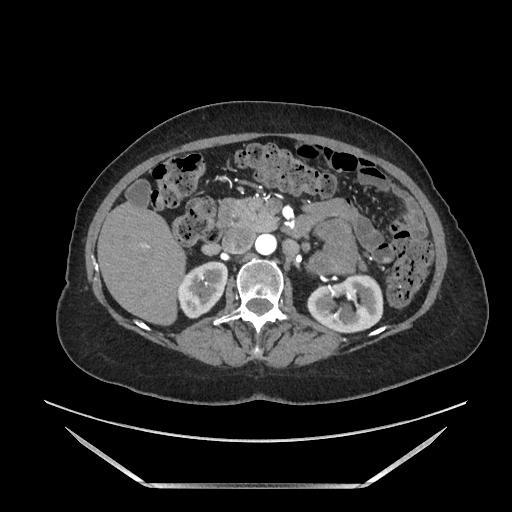
Contrast-enhanced abdominal CT, one axial slice. Position 86 of 205 along the scan axis. Soft-tissue window (W 400 / L 40 HU). 512 × 512 image matrix. Female patient. From the clinical record (not read from this slice): diagnosis: adrenocortical carcinoma; tumour side: left adrenal; tumour size at pathology: 12.5 cm; Ki-67 index: 39 %; stage (as recorded): 3.
Annotated regions visible in this slice (semi-automatic segmentation, software-assisted and operator-edited):
- mass: box from (x=313, y=221) to (x=365, y=273) px